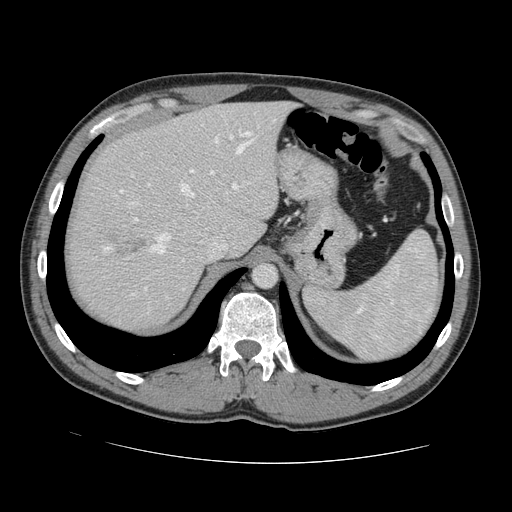
Contrast-enhanced abdominal CT, one axial slice. Position 102 of 131 along the scan axis. Intravenous contrast given. Soft-tissue window (W 400 / L 40 HU). 2.5 mm slice thickness. 512 × 512 image matrix, field of view 380 × 380 mm. Male patient, age 40 years. Case-level facts recorded for this patient, not image findings: diagnosis: colorectal cancer liver metastases, imaged before liver resection; multiple liver metastases: yes; largest metastasis: 2.9 cm.
Annotated regions visible in this slice (manually delineated by an expert):
- hepatic veins: bounding box (x1, y1, x2, y2) in pixels: (151, 138, 250, 254)
- liver: (70, 102, 290, 330)
- planned liver remnant (the part of the liver to remain after resection): (97, 101, 289, 255)
- portal vein (with intrahepatic branches): (190, 132, 252, 190)
- liver metastasis: (119, 238, 145, 255)